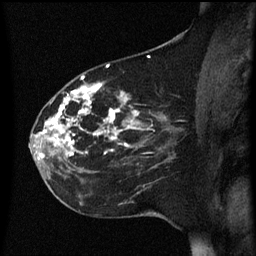
Breast MRI (dynamic contrast-enhanced), one sagittal slice; slice 25 of 60 in the series (ordered by position); dynamic contrast-enhanced series, image 2 of 3 at this slice position (ordered by acquisition); 1.5 T; TE 4.2 ms, TR 8.4 ms; 256 × 256 image matrix. Patient: female, 35 years. Case-level facts recorded for this patient, not image findings: setting: breast cancer imaged before/during neoadjuvant chemotherapy; receptor status: HER2-positive.
Annotated regions visible in this slice (semi-automatic segmentation, software-assisted and operator-edited):
- analysis volume of interest (the breast-tissue region the enhancement analysis was run in; not a lesion): bounding box (x1, y1, x2, y2) in pixels: (32, 78, 173, 163)
- tumour enhancement mask (voxels above the 70 % enhancement threshold inside the analysis volume of interest): (37, 78, 143, 157)